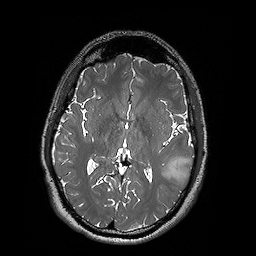
Brain MRI from a brain-tumour surgery series, one axial slice; 256 × 256 image matrix, field of view 250 × 250 mm. Case-level facts recorded for this patient, not image findings: histopathology: Oligodendroglioma; WHO grade: 2; IDH mutation: yes.
Structures marked on this image (expert manual segmentation):
- tumour: bounding box <159,155,193,180> (left, top, right, bottom; pixels)